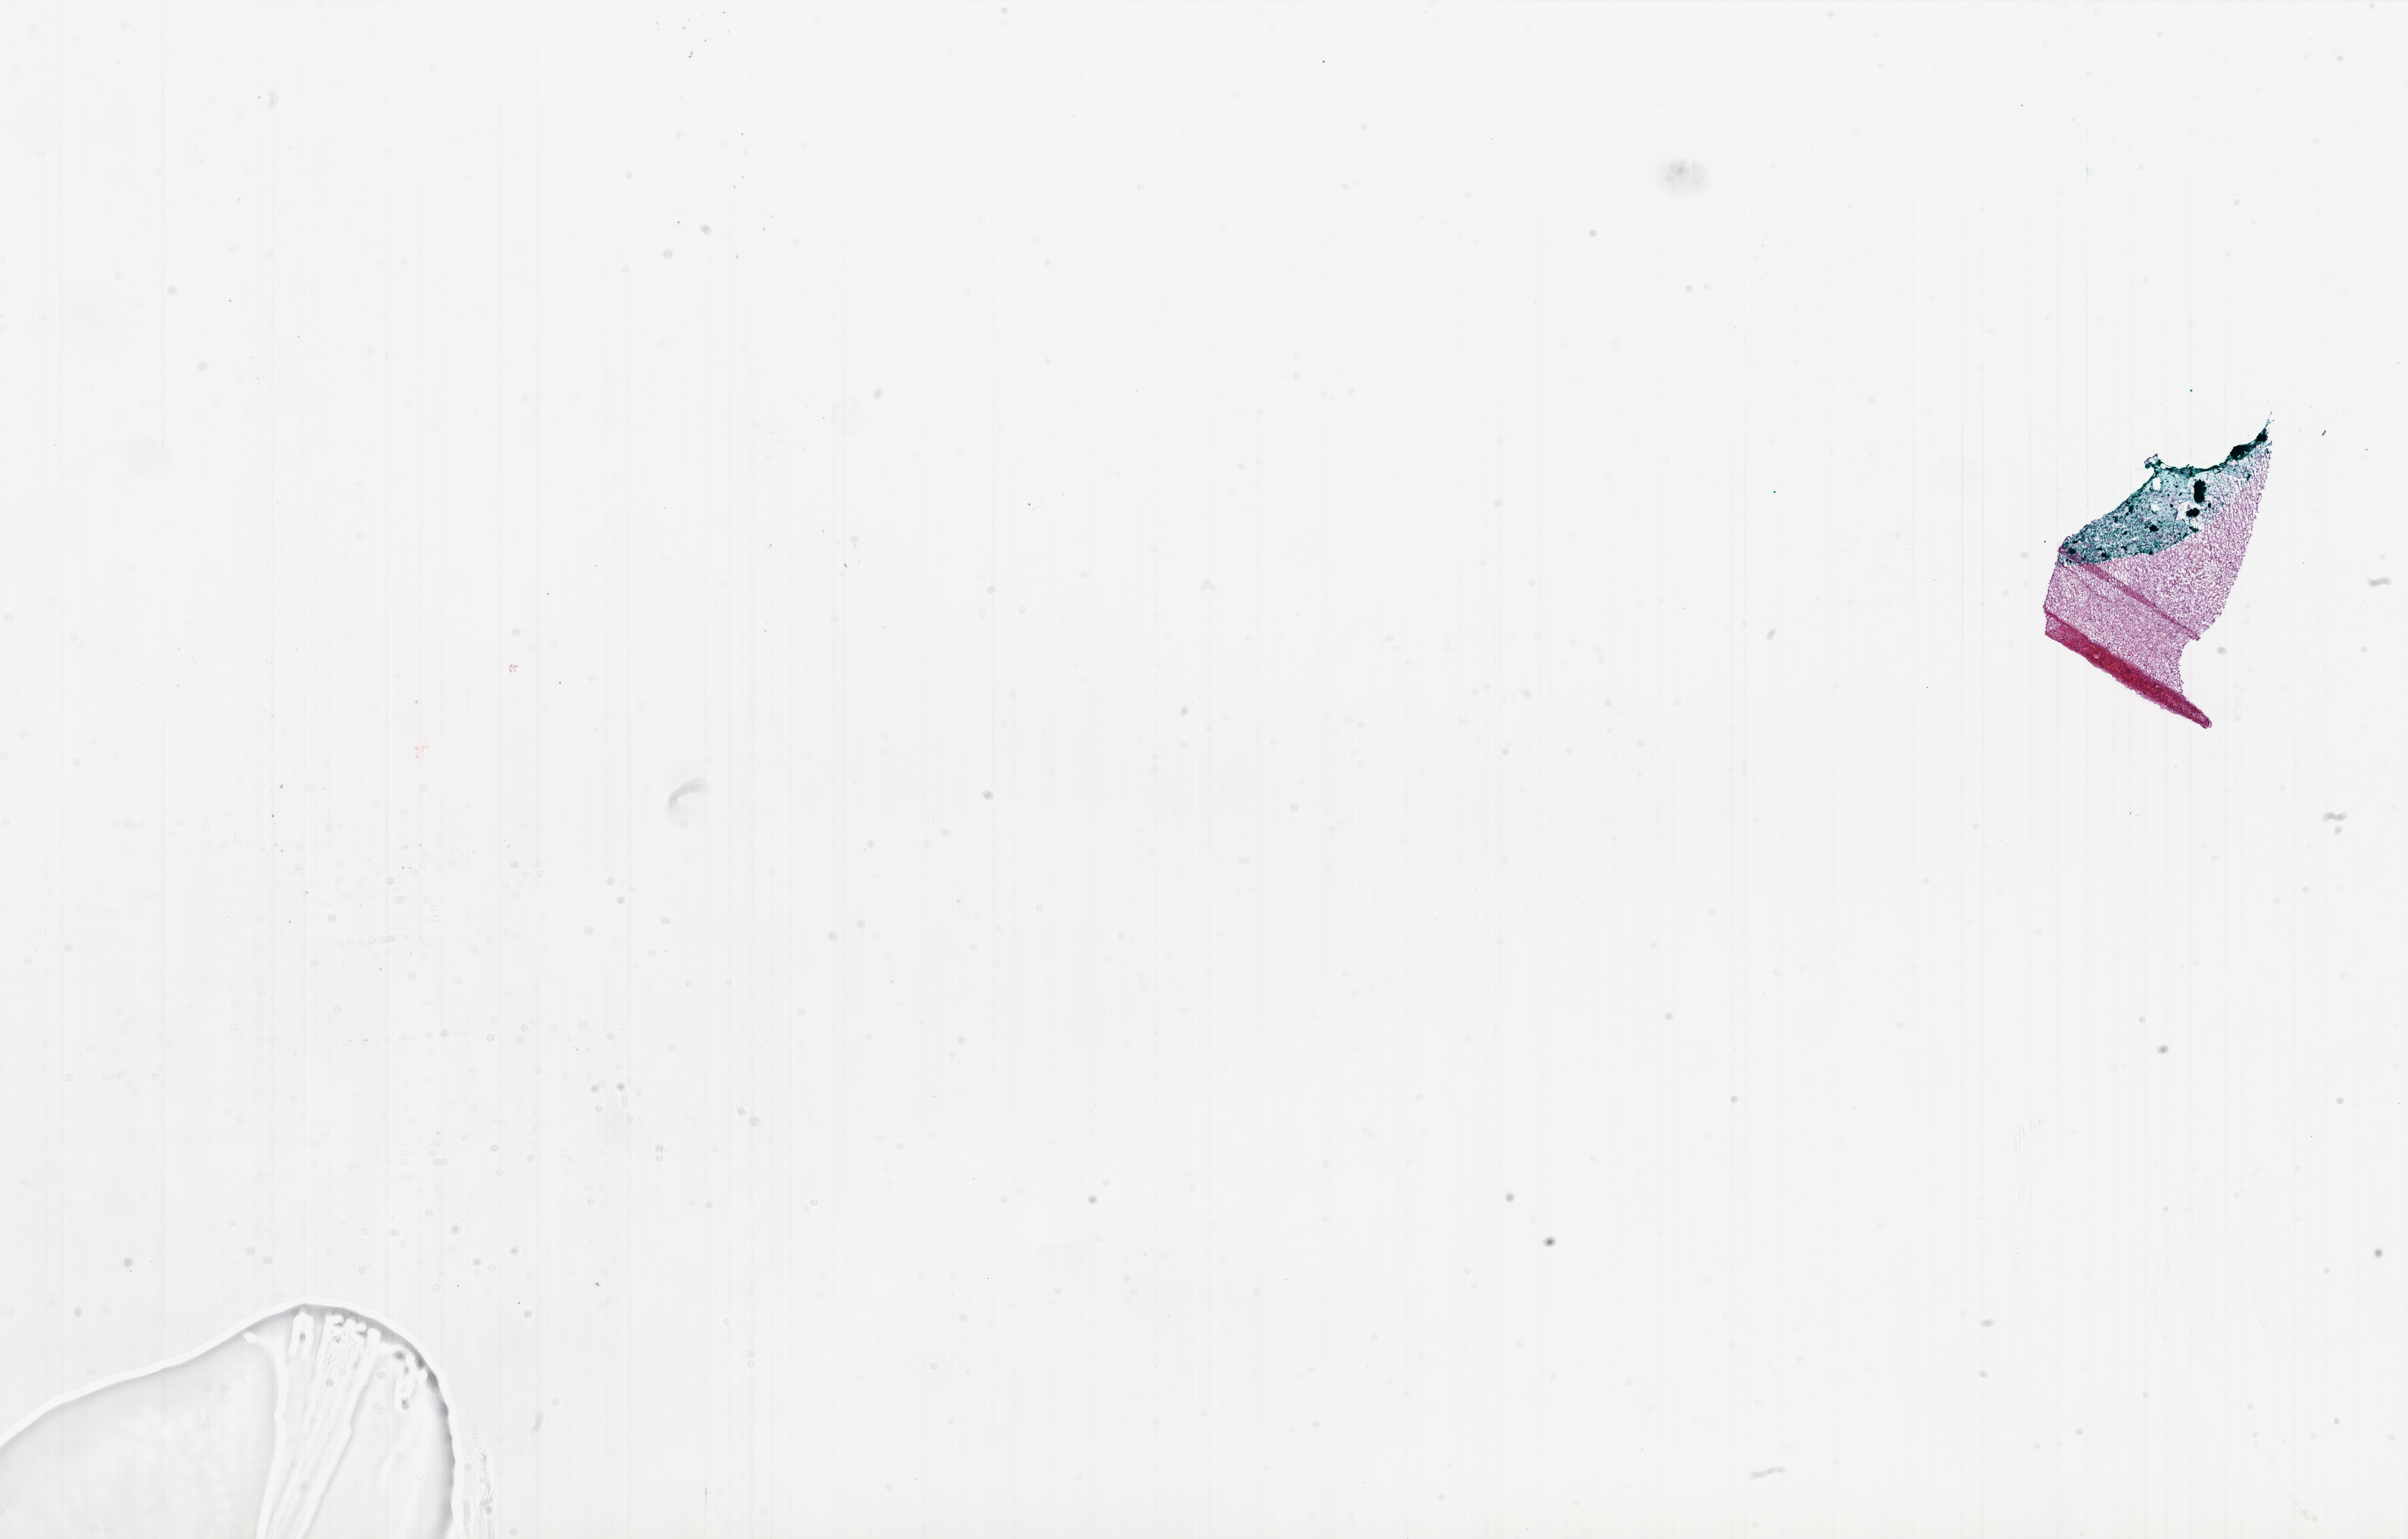
Hematoxylin and eosin (H&E) stained whole-slide image — low-resolution overview of the scanned area, about 30.0 x 19.2 mm (from a 20x scan), frozen section from the bottom of the tissue portion, sample: primary tumour, brain. Male, age 51 years at initial diagnosis. Slide review estimates, as recorded: tumour cells 75%, tumour nuclei 80%, normal cells 0%, stromal cells 25%, necrosis 0%.
Diagnosis: Glioblastoma.